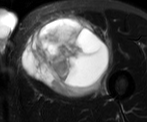
MRI of an extremity soft-tissue mass, one axial slice. T2-weighted fat-saturated. MR volume resampled by the dataset authors to the PET/CT grid (not the native acquisition matrix). 147 × 122 image matrix. Male patient. Case-level facts recorded for this patient, not image findings: histological type: pleiomorphic liposarcoma; grade: high; site of the primary tumour: left thigh.
Outlined on this slice (expert contour drawn on MRI and transferred to this co-registered scan by the dataset authors):
- gross tumour volume including surrounding oedema: bounding box (x1, y1, x2, y2) in pixels: (23, 18, 111, 93)
- gross tumour volume (mass): (23, 18, 108, 93)